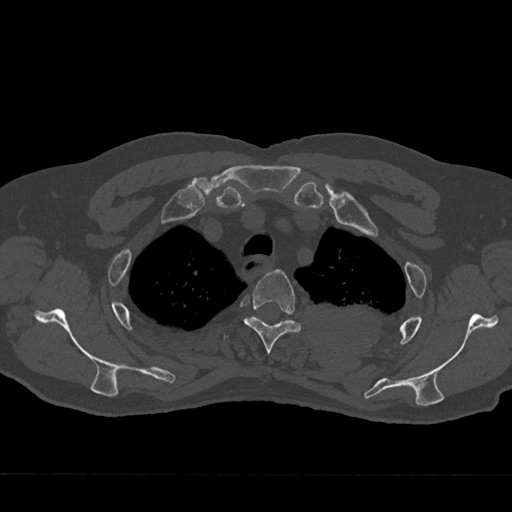
CT including the spine, one axial slice. Slice 566 of 797 in the series (ordered by position). Reconstruction kernel Br40s/3. 120 kVp. Bone window (W 1800 / L 400 HU). 0.5 mm slice thickness. 512 × 512 image matrix, field of view 377 × 377 mm. Male patient, age 75 years. Case-level facts recorded for this patient, not image findings: primary cancer: renal; vertebrae with lytic lesions (as recorded): T4.
Structures marked on this image (semi-automatic segmentation, software-assisted and operator-edited):
- T3 vertebra: bounding box (x1, y1, x2, y2) in pixels: (243, 269, 302, 354)